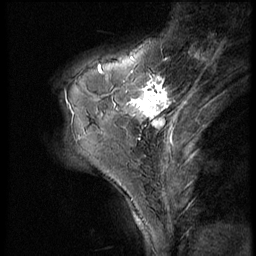
Breast MRI (dynamic contrast-enhanced), one sagittal slice. 3 images stored at this slice position (order not interpretable as contrast timing). 1.5 T. TE 4.2 ms, TR 9 ms. 2.5 mm slice thickness. 256 × 256 image matrix. Patient: female, 46 years. Case-level facts recorded for this patient, not image findings: setting: breast cancer imaged before/during neoadjuvant chemotherapy; receptor status: HER2-positive.
Outlined on this slice (semi-automatically segmented with operator editing):
- analysis volume of interest (the breast-tissue region the enhancement analysis was run in; not a lesion): bounding box [x1, y1, x2, y2] px = [79, 68, 190, 143]
- tumour enhancement mask (voxels above the 140 % enhancement threshold inside the analysis volume of interest): [99, 68, 177, 130]